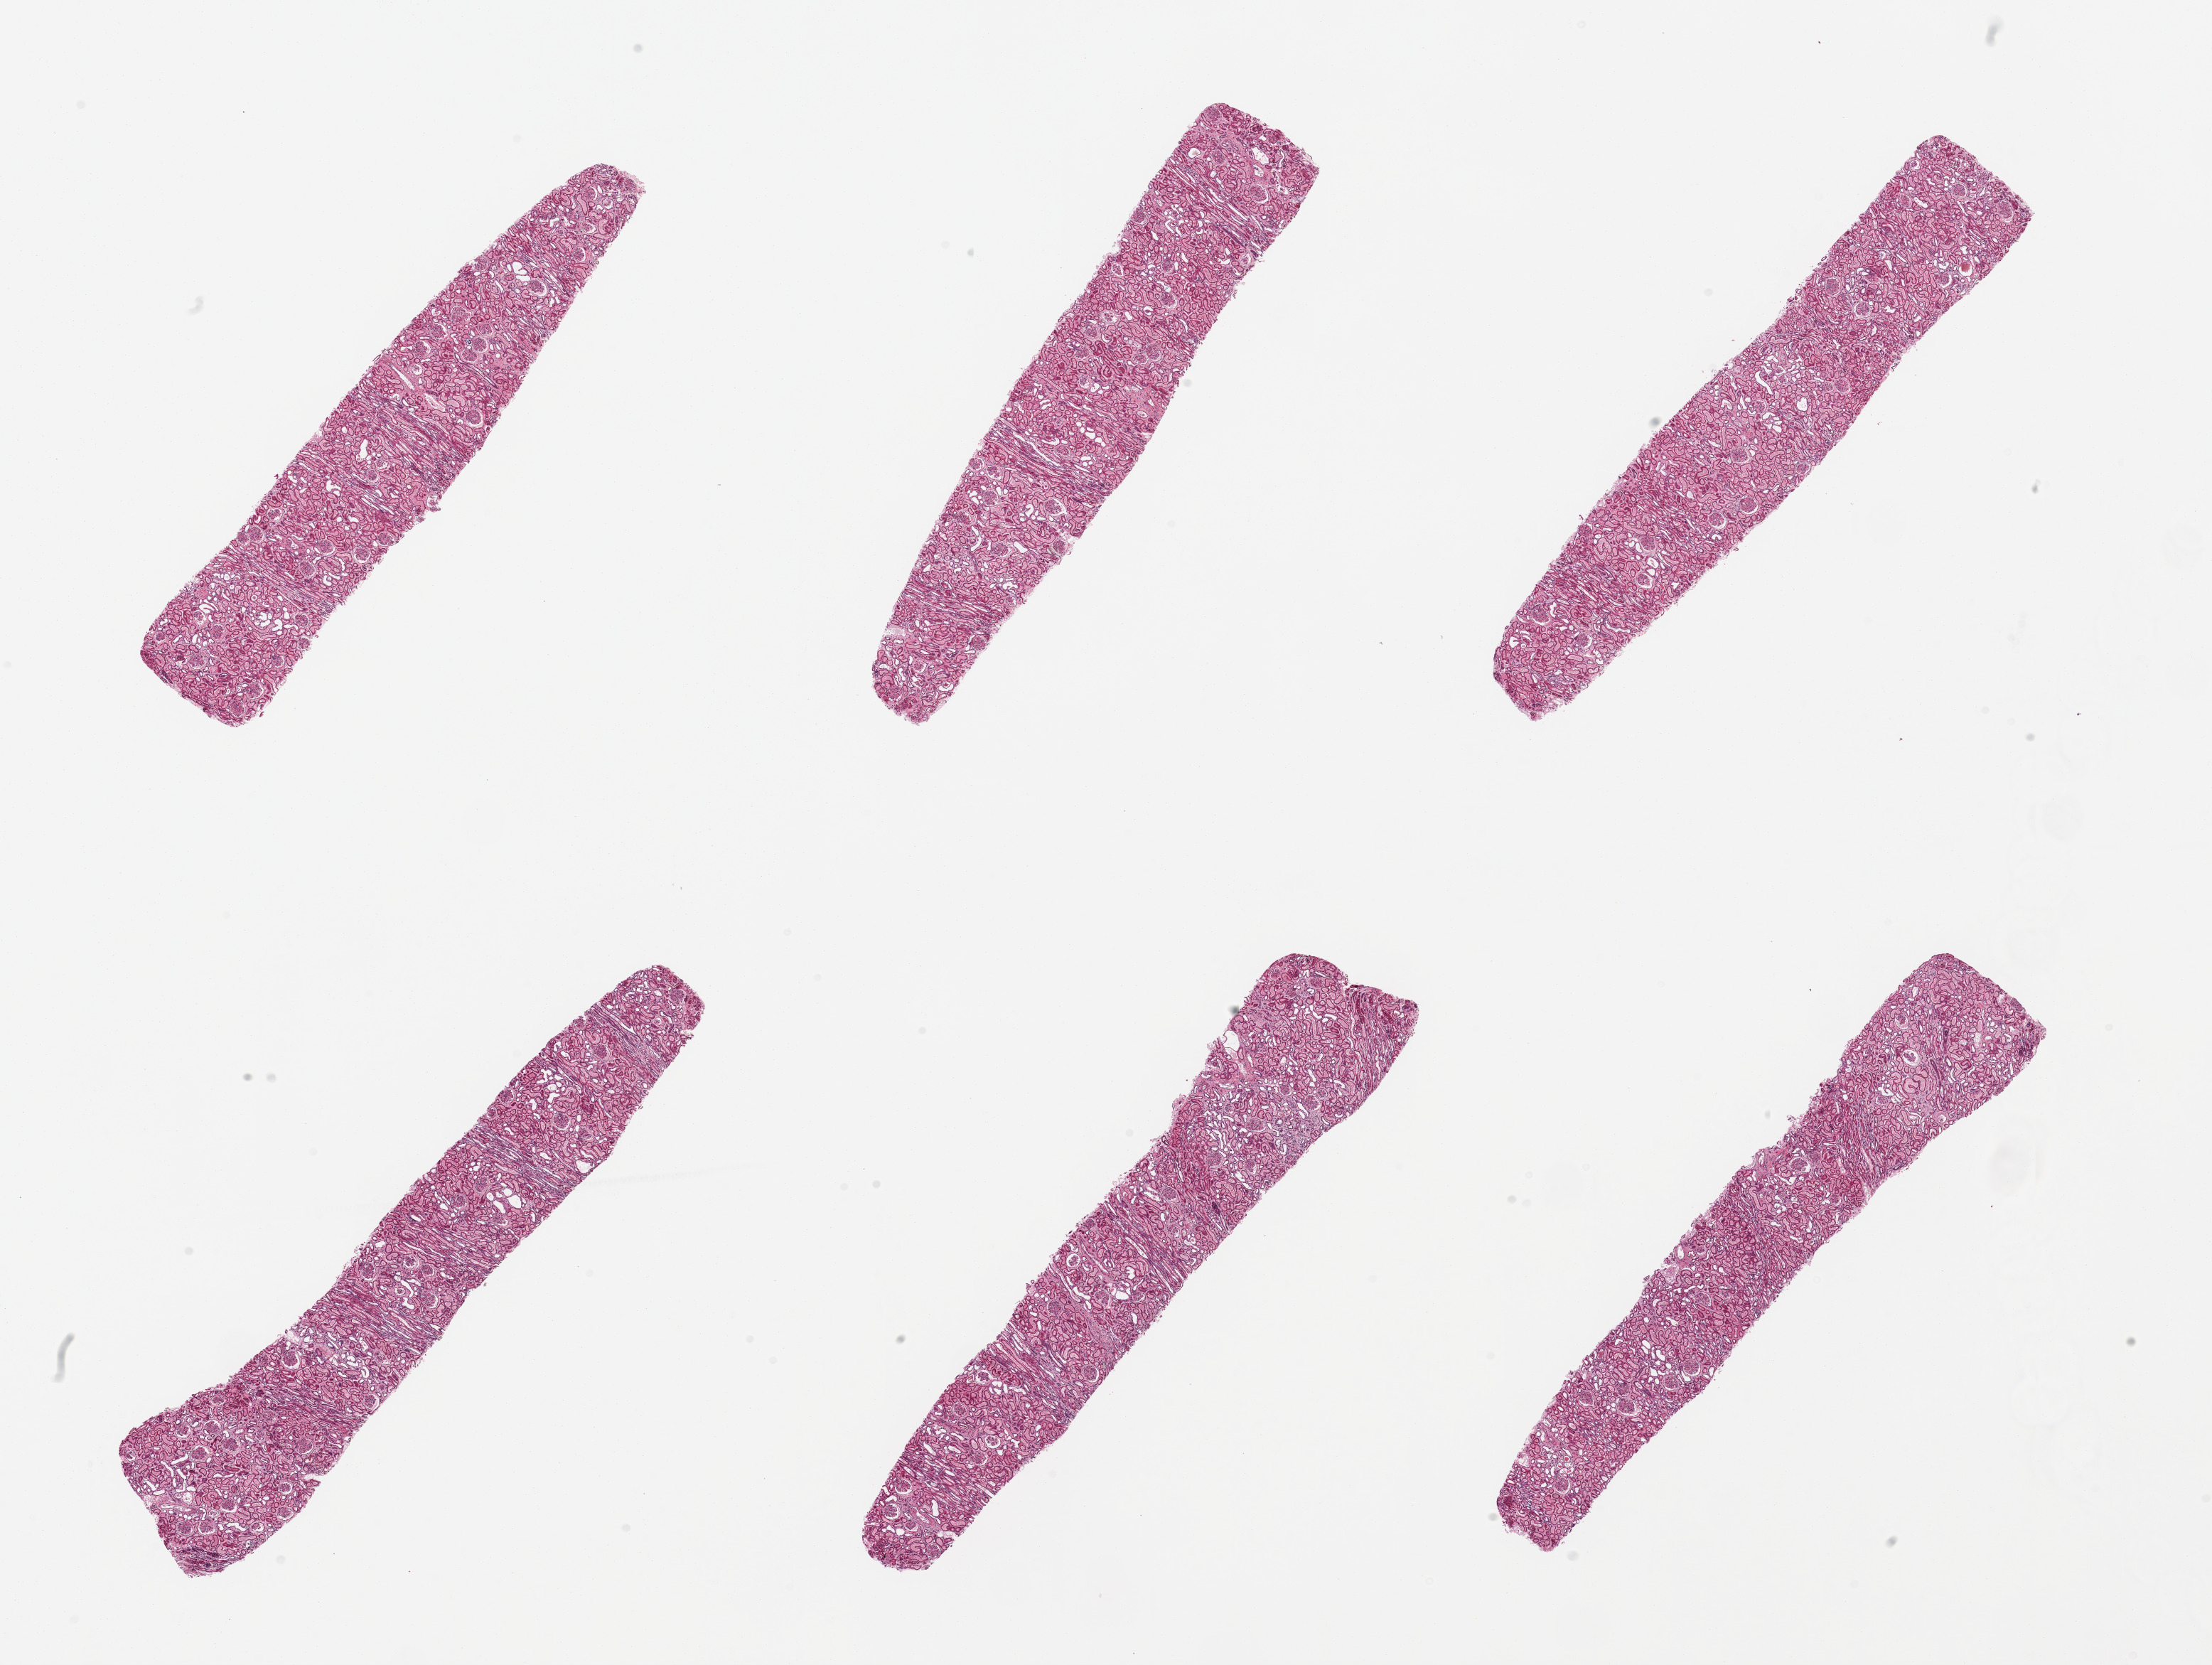
Whole-slide image, hematoxylin and eosin (H&E) stain — low-resolution overview of the scanned area, about 24.6 x 18.5 mm (slide scanned at 20x); PAXgene-fixed paraffin-embedded (PFPE) section; target tissue: renal cortex; donor tissue sample.
Reviewer comment on this tissue sample: 6 pieces, tubules unusually well preserved. Glomeruli present.